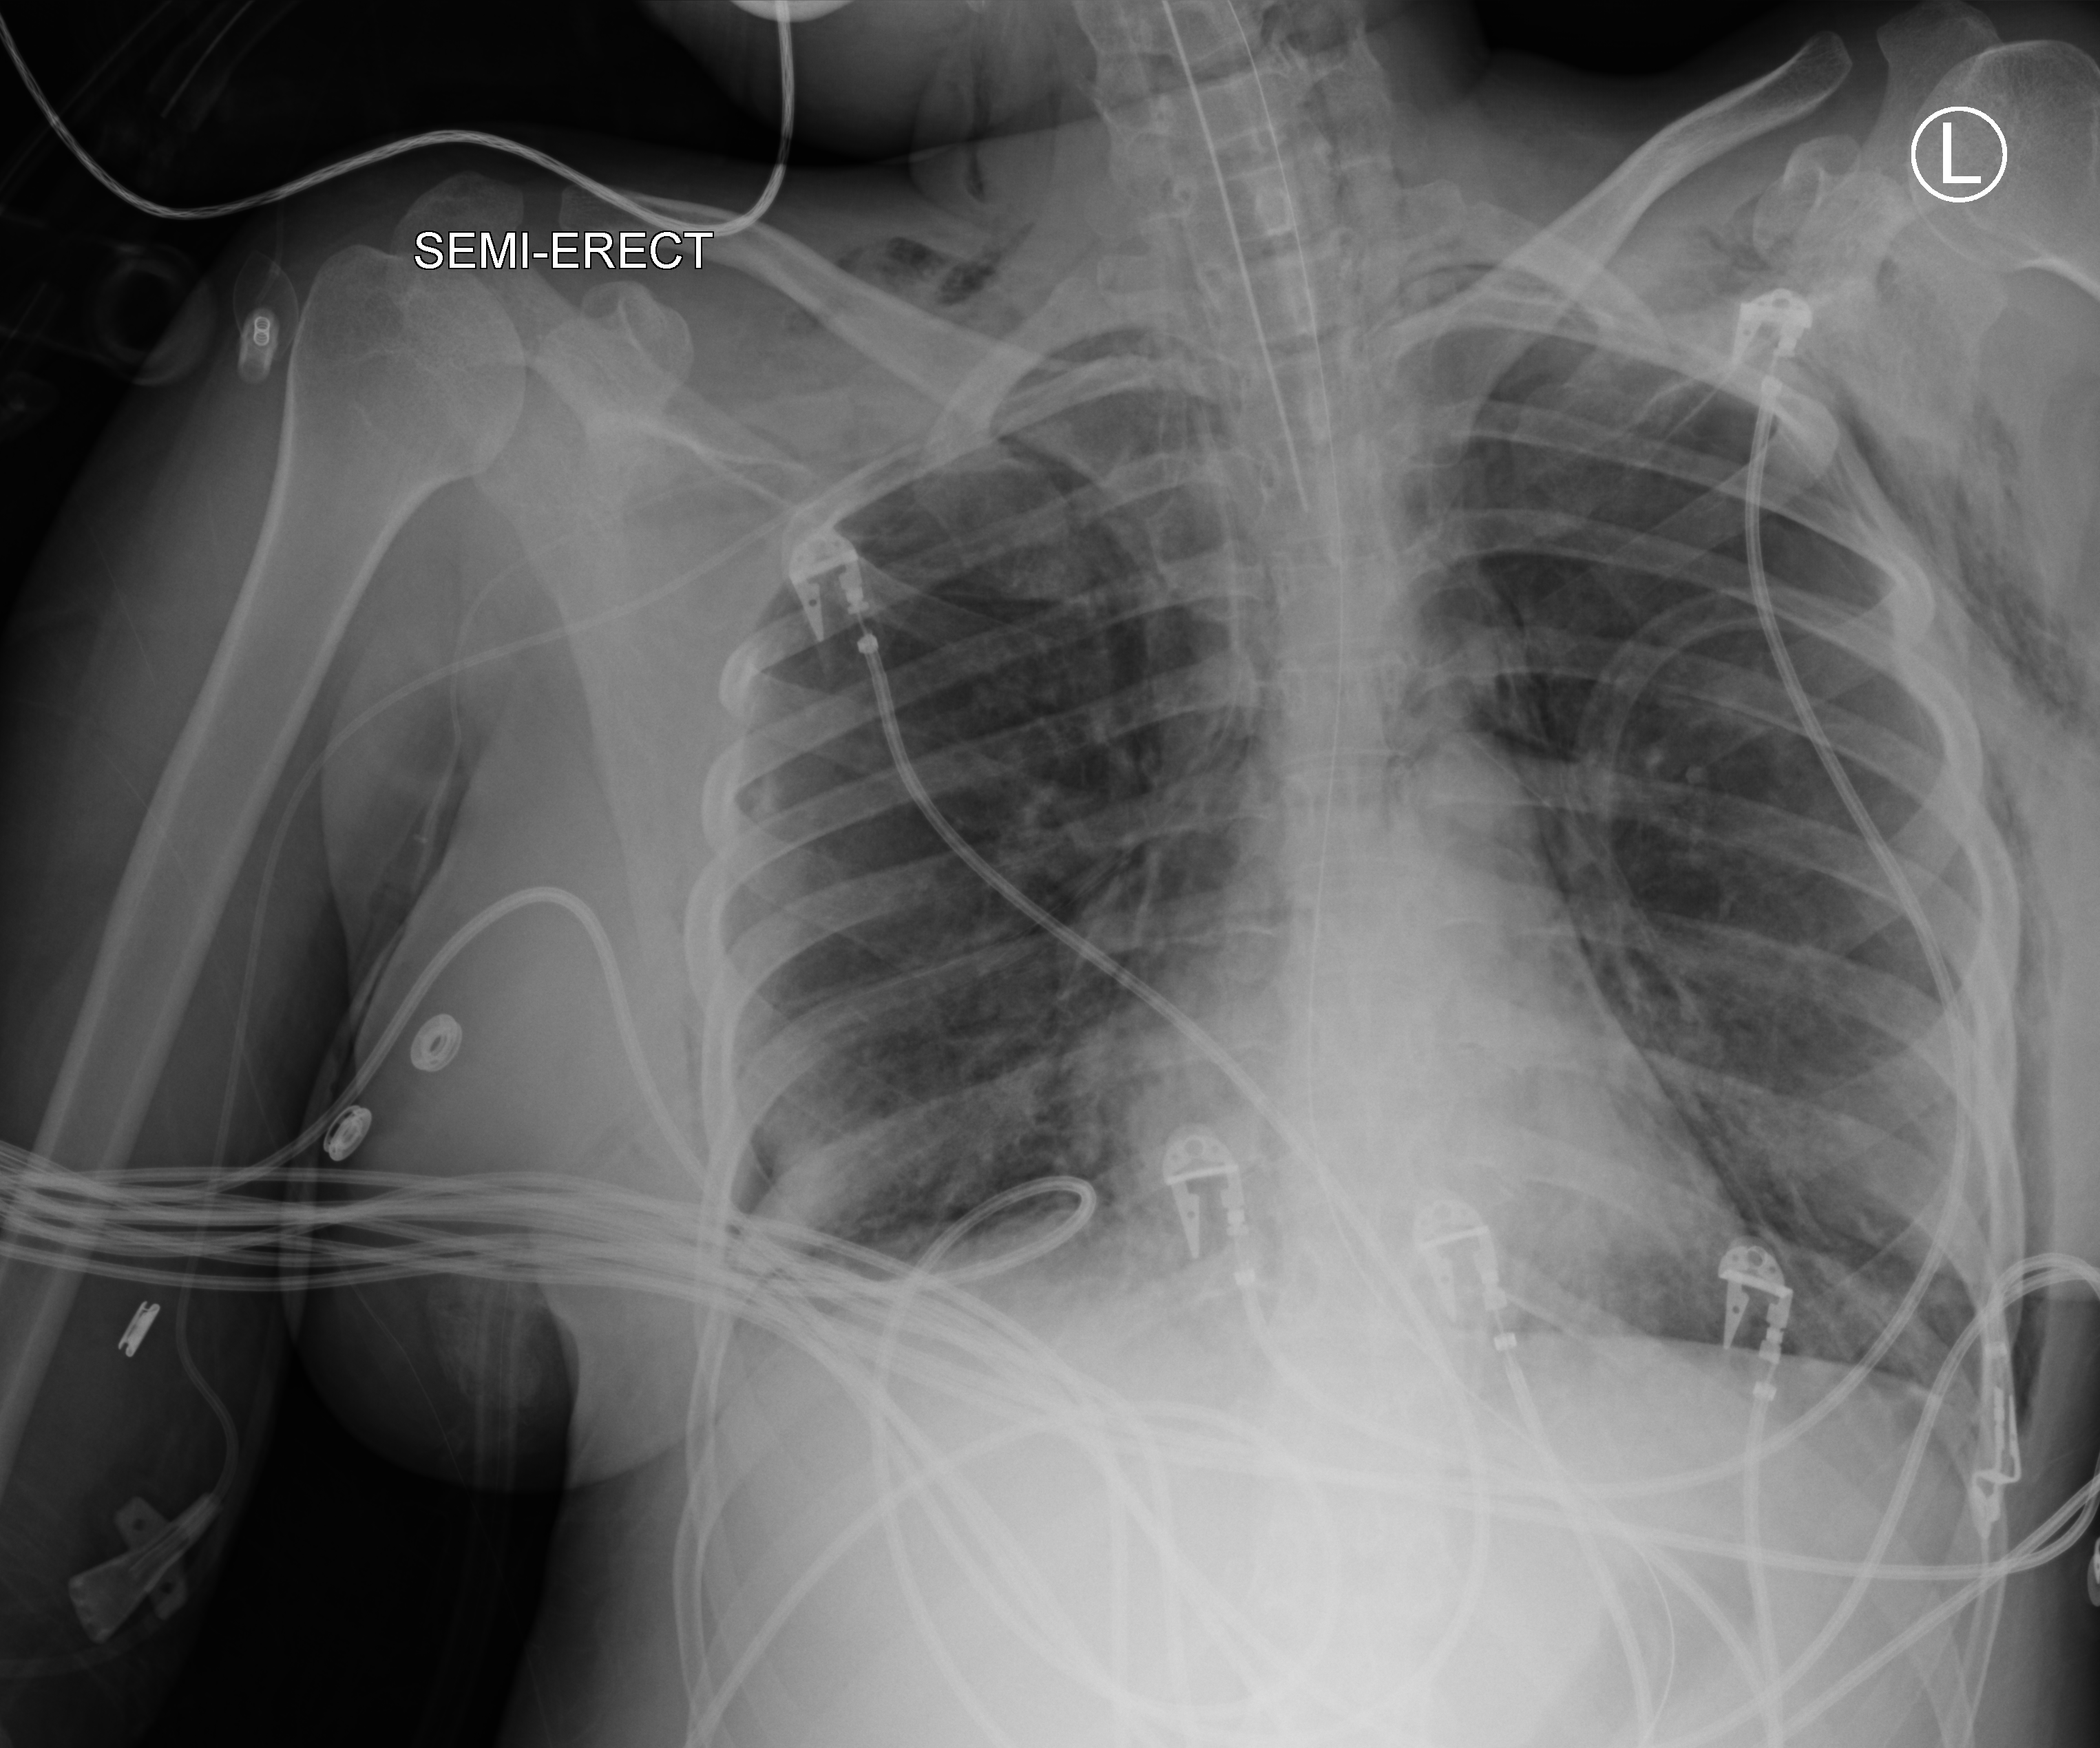
Bedside chest radiograph (computed radiography), anteroposterior (AP) projection. Adult patient hospitalised with COVID-19, age 18–59 years.
Admission-level facts for this patient (not findings on this image; timing relative to this image not recorded): admitted to intensive care during this hospital stay: yes; COPD (admission record): no; mechanically ventilated during this hospital stay: yes.